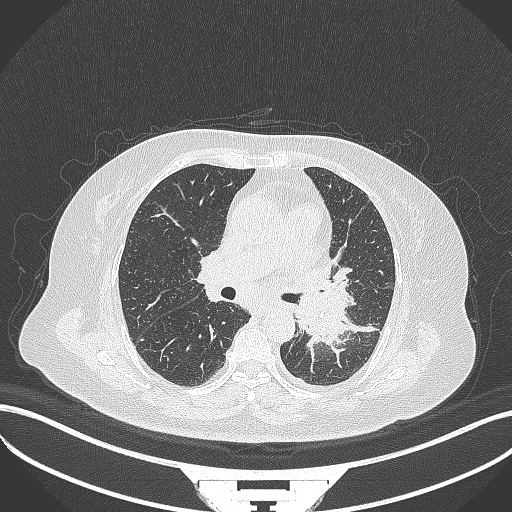
Chest CT, one axial slice; slice 197 of 322 in the series (ordered by position); reconstruction kernel B70f; lung window (W 1500 / L -600 HU); 1 mm slice thickness; 512 × 512 image matrix, field of view 400 × 400 mm. Patient: female, 69 years. Case-level facts recorded for this patient, not image findings: clinical TNM (as recorded): T2b N3 M1.
Outlined on this slice (bounding box drawn by a radiologist):
- lung tumour (recorded histology: adenocarcinoma): bounding box (x1, y1, x2, y2) in pixels: (293, 281, 356, 346)